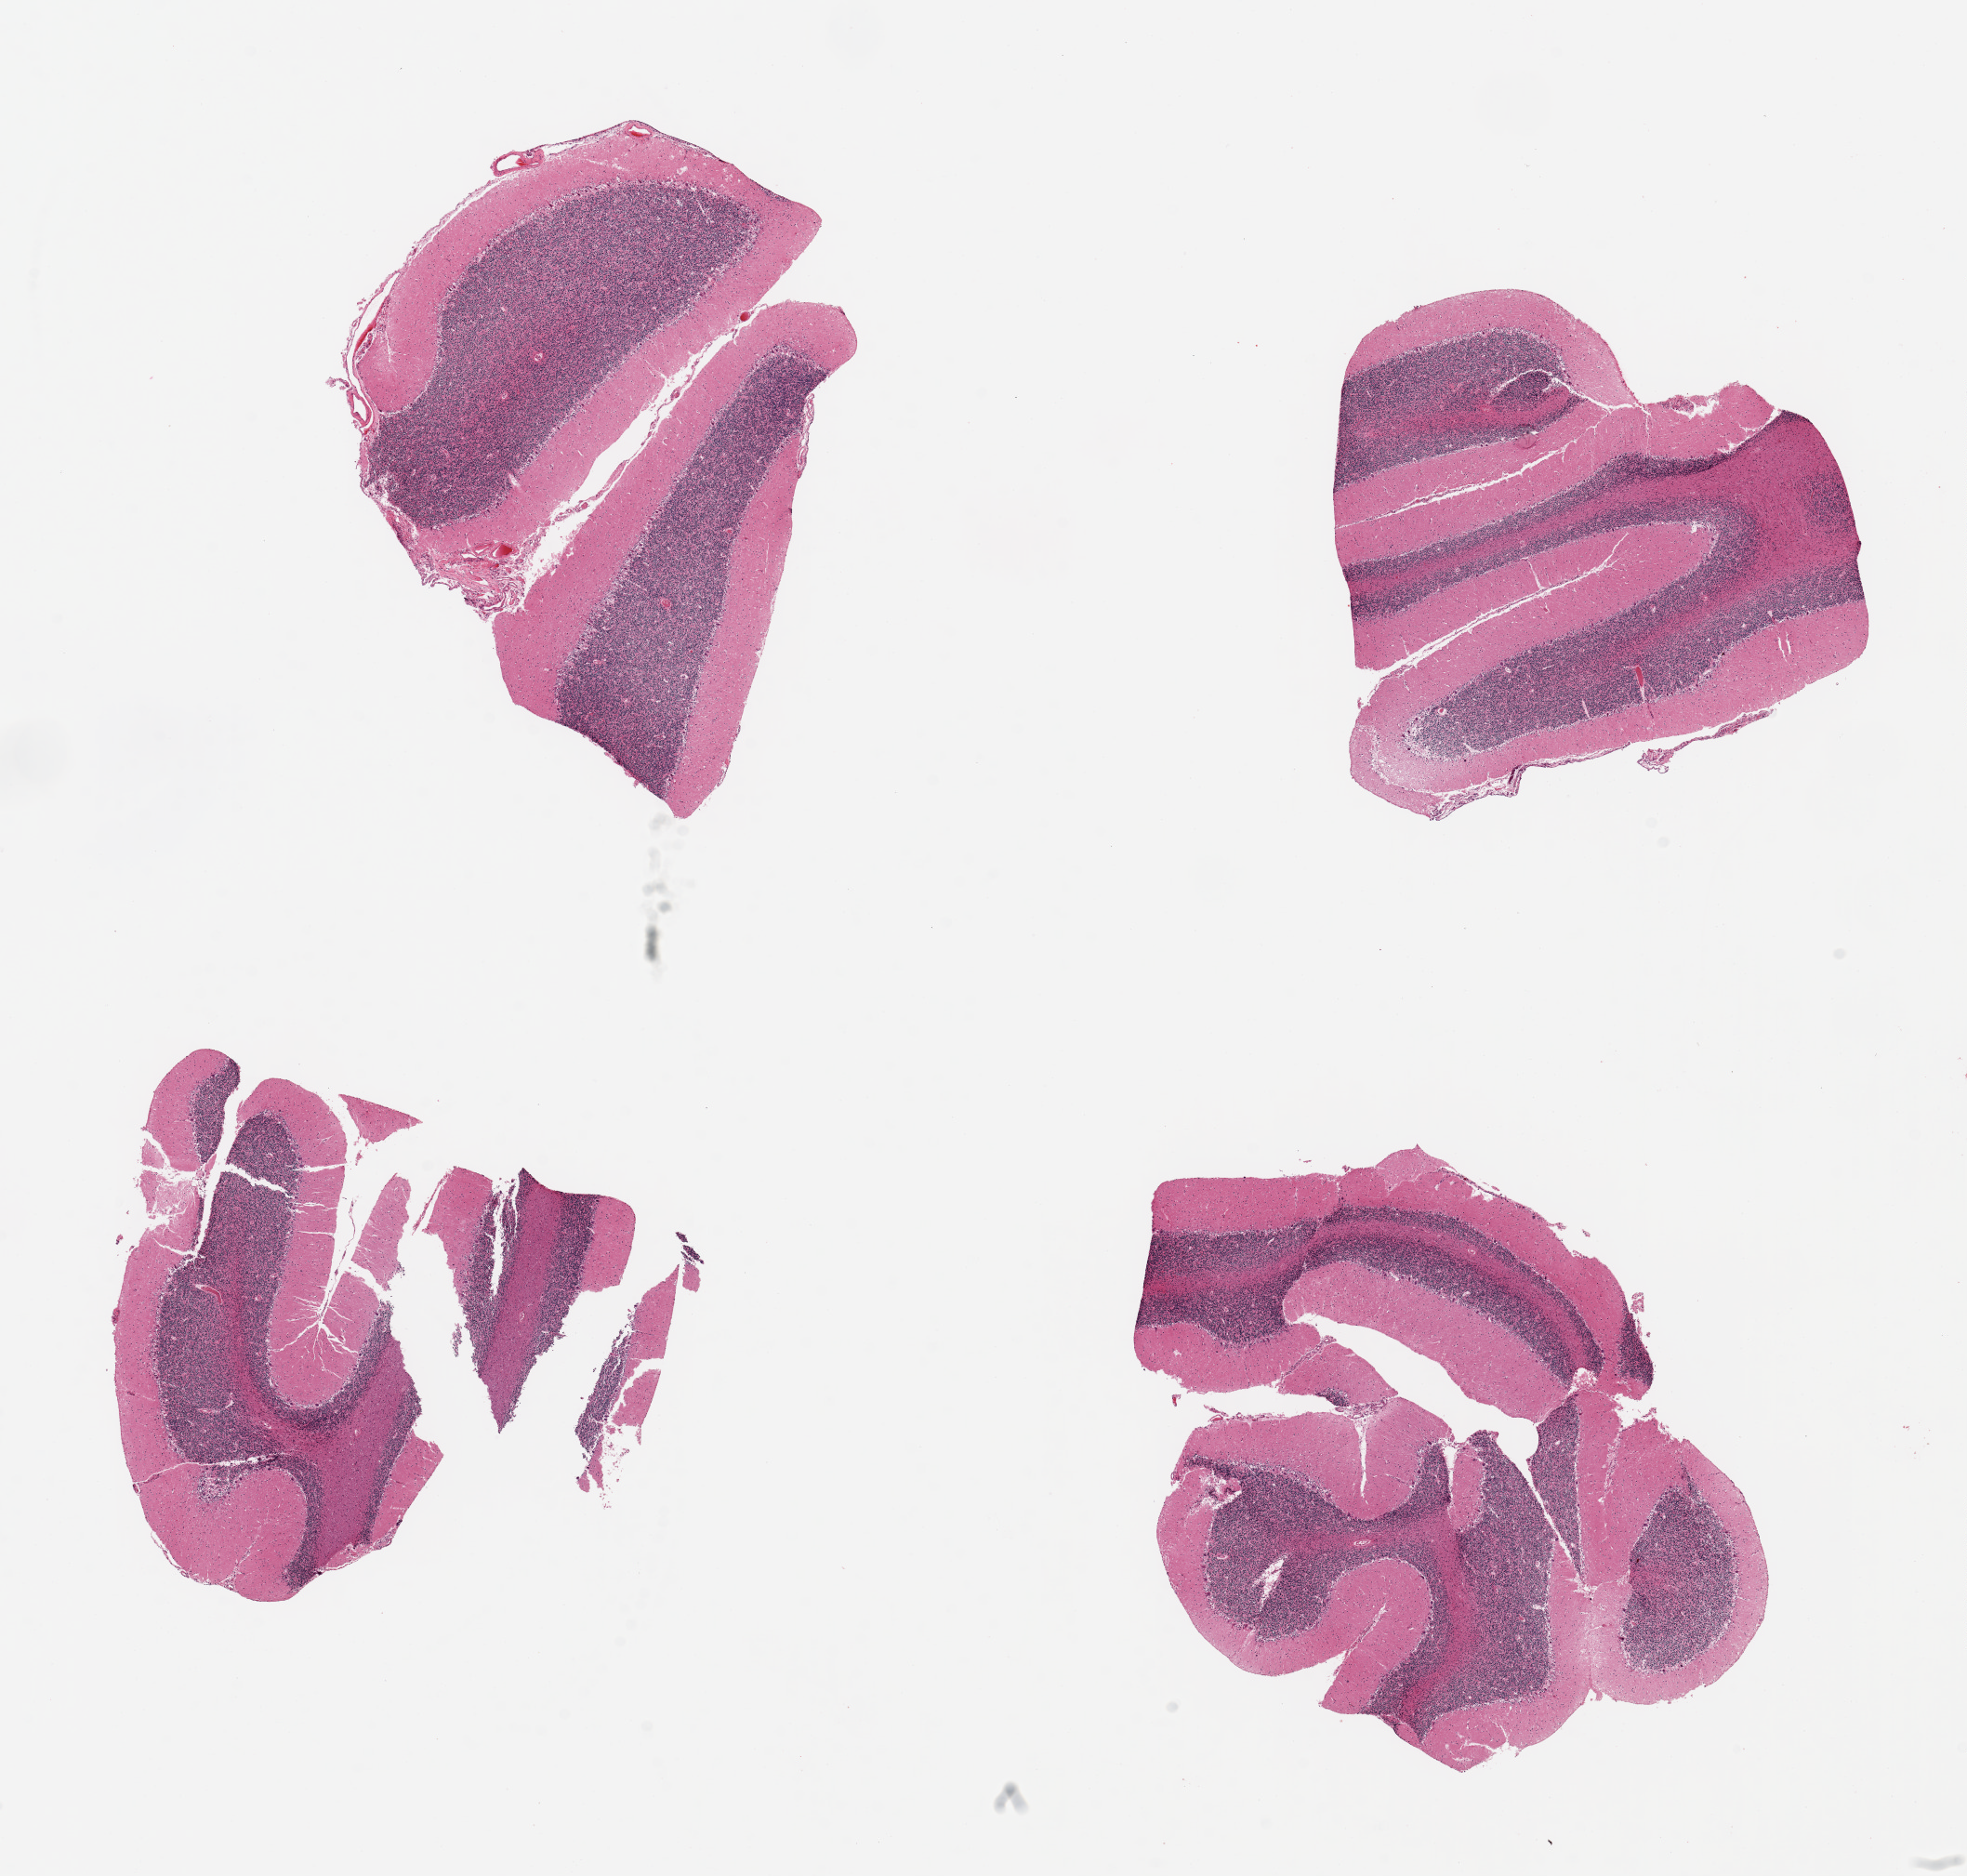
Whole-slide image, hematoxylin and eosin (H&E) stain — low-resolution overview of the scanned area, about 16.7 x 16.0 mm (from a 20x scan), PAXgene-fixed, paraffin-embedded tissue, sampled site (target tissue): cerebellum, tissue donor sample.
• review note (as recorded): 4pieces, ~5x4mm. Granular layer more autolyzed